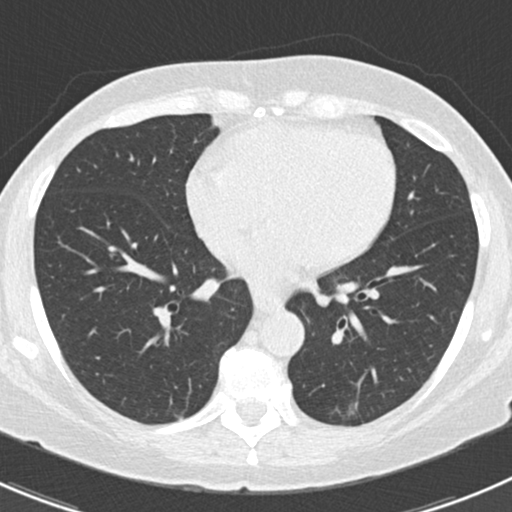
Low-dose screening chest CT, one axial slice; position 78 of 166 along the scan axis; reconstruction kernel B30f; lung window (W 1500 / L -600 HU); 512 × 512 image matrix, field of view 307 × 307 mm.
Annotated regions visible in this slice (manually delineated by an expert):
- lesion 1 (tumor, lower lobe of left lung): bounding box (x1, y1, x2, y2) in pixels: (347, 401, 359, 417)